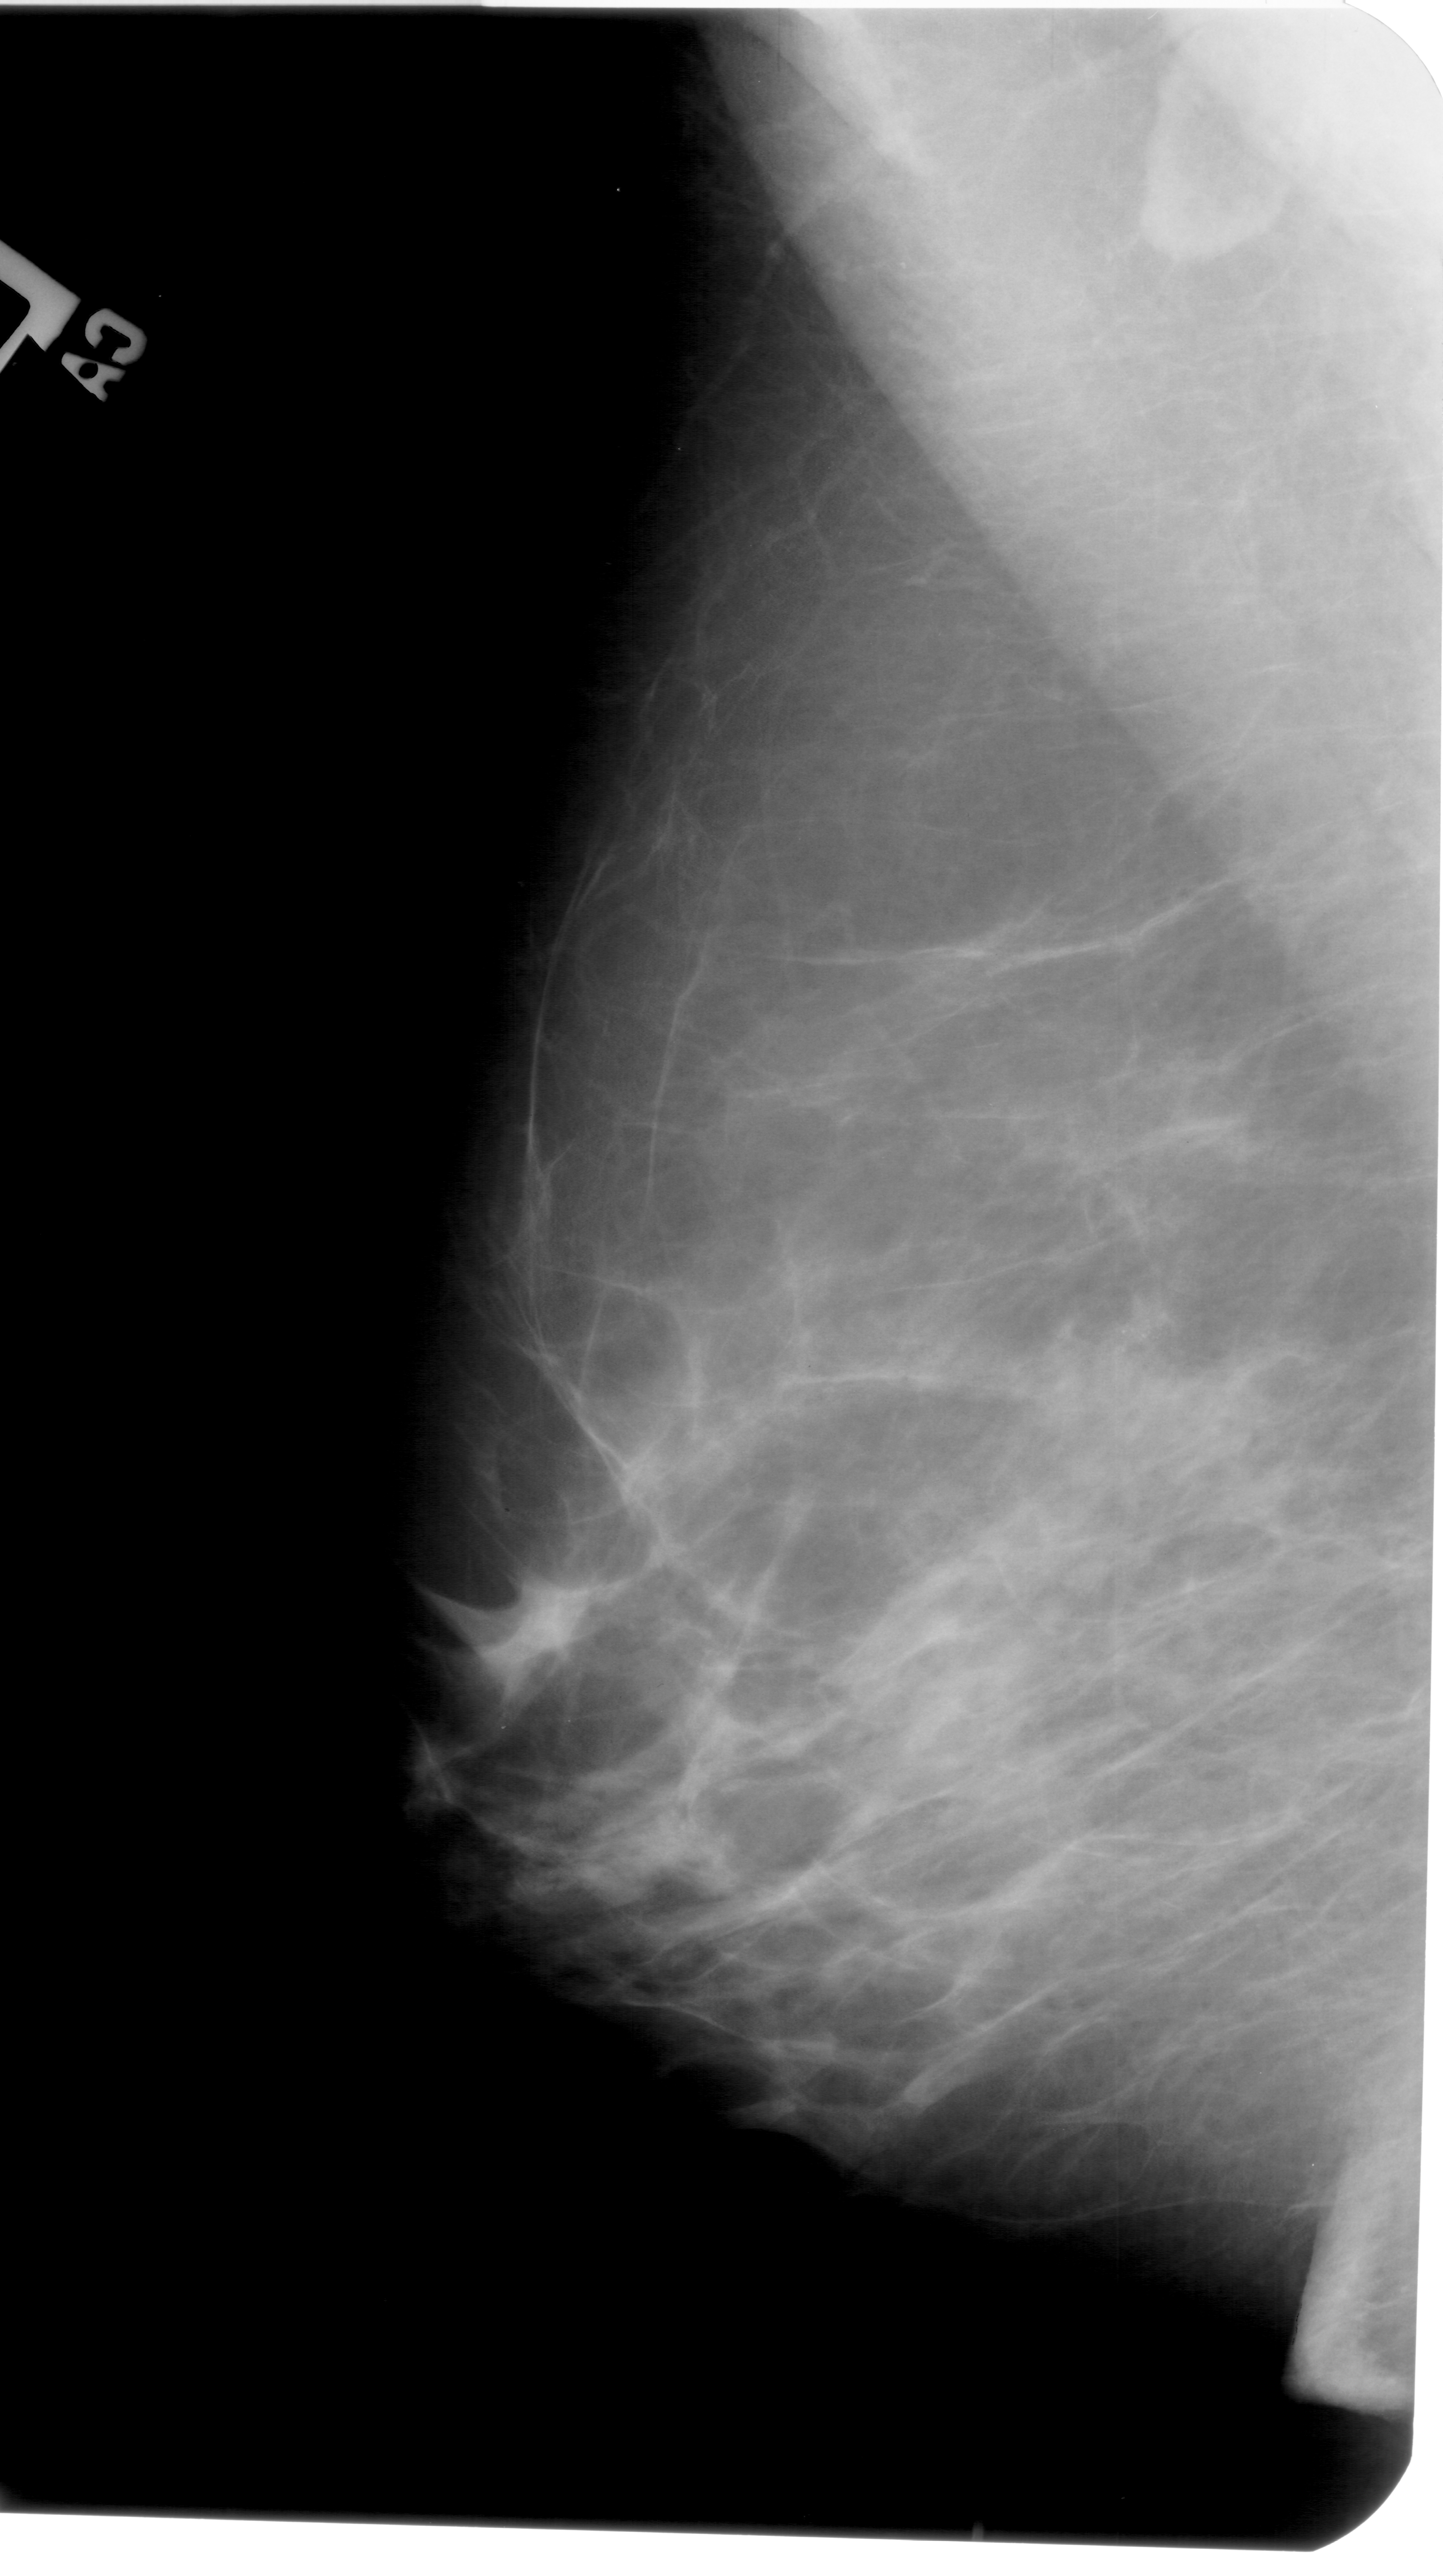
Mammogram (digitized film), left breast, mediolateral oblique (MLO) view.
Abnormality record for this image: calcifications, morphology pleomorphic, distribution clustered; BI-RADS assessment category 4; subtlety rating 2 on a 1 (subtle) to 5 (obvious) scale; pathology (as recorded): benign.